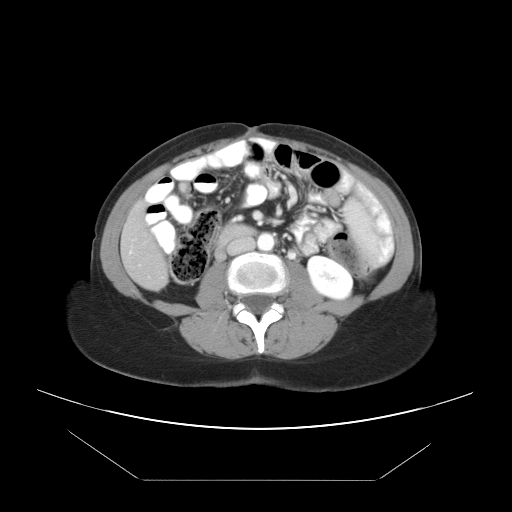
Contrast-enhanced abdominal CT, one axial slice; position 9 of 45 along the scan axis; reconstruction kernel STANDARD; 120 kVp; intravenous contrast given; soft-tissue window (W 400 / L 40 HU); 5 mm slice thickness; 512 × 512 image matrix, field of view 405 × 405 mm. Female patient, age 52 years. From the clinical record (not read from this slice): diagnosis: colorectal cancer liver metastases, imaged before liver resection; multiple liver metastases: yes; largest metastasis: 2.5 cm; disease in both lobes: no.
Outlined on this slice (expert manual segmentation):
- liver: bounding box [x1, y1, x2, y2] px = [122, 208, 166, 289]
- planned liver remnant (the part of the liver to remain after resection): [123, 208, 158, 258]